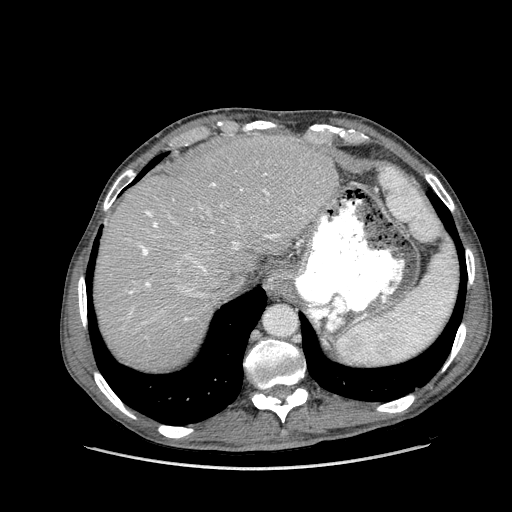
Contrast-enhanced abdominal CT (liver protocol), one axial slice. Position 119 of 162 along the scan axis. 100 kVp. Soft-tissue window (W 400 / L 40 HU). 2.5 mm slice thickness. 512 × 512 image matrix, field of view 400 × 400 mm. Case-level facts recorded for this patient, not image findings: diagnosis: hepatocellular carcinoma (patient treated with transarterial chemoembolisation; whether this scan precedes or follows treatment is not stated here); TNM stage (as recorded): Stage-IIIA; Child-Pugh class: A; tumour nodularity: multinodular.
Outlined on this slice (semi-automatically segmented with operator editing):
- abdominal aorta: bounding box (x1, y1, x2, y2) in pixels: (265, 305, 296, 336)
- liver parenchyma outside the tumour (the mass and vessels are separate outlines, so this box may not span the whole liver): (94, 134, 338, 370)
- liver vessels: (129, 173, 305, 320)